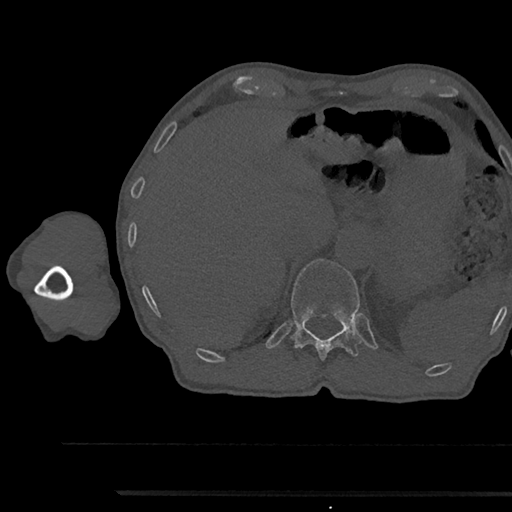
CT including the spine, one axial slice. Position 716 of 797 along the scan axis. Bone window (W 1800 / L 400 HU). 0.5 mm slice thickness. 512 × 512 image matrix, field of view 367 × 367 mm. Patient: male, 79 years. Case-level facts recorded for this patient, not image findings: primary cancer: prostate.
Structures marked on this image (semi-automatic segmentation, software-assisted and operator-edited):
- T12 vertebra: bounding box [x1, y1, x2, y2] px = [284, 258, 364, 361]